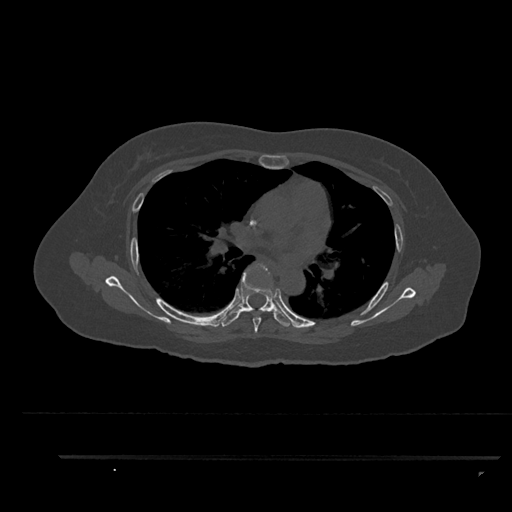
CT including the spine, one axial slice. Position 576 of 797 along the scan axis. Reconstruction kernel Br40s/3. Bone window (W 1800 / L 400 HU). 0.5 mm slice thickness. 512 × 512 image matrix, field of view 408 × 408 mm. Patient: female, 44 years. From the clinical record (not read from this slice): primary cancer: renal; vertebrae with lytic lesions (as recorded): L1.
Annotated regions visible in this slice (semi-automatically segmented with operator editing):
- T5 vertebra: box from (x=252, y=264) to (x=270, y=333) px
- T6 vertebra: (x=221, y=264)–(x=295, y=328)